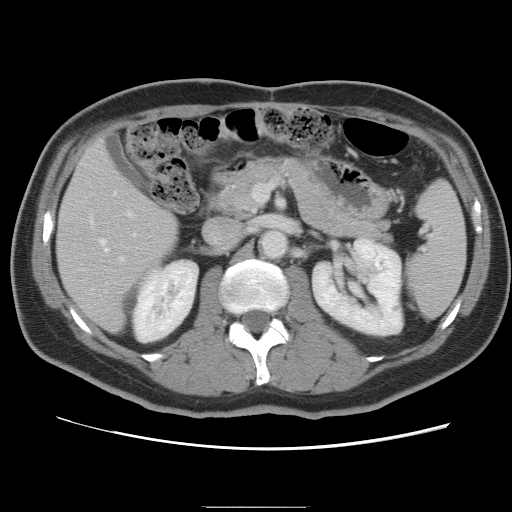
Contrast-enhanced abdominal CT, one axial slice; 120 kVp; intravenous contrast given; soft-tissue window (W 400 / L 40 HU); 5 mm slice thickness; 512 × 512 image matrix. Male patient, age 63 years. From the clinical record (not read from this slice): diagnosis: colorectal cancer liver metastases, imaged before liver resection; multiple liver metastases: no; largest metastasis: 9 cm.
Outlined on this slice (expert manual segmentation):
- hepatic veins: bounding box (x1, y1, x2, y2) in pixels: (100, 192, 116, 251)
- liver: (58, 142, 177, 332)
- planned liver remnant (the part of the liver to remain after resection): (58, 143, 177, 332)
- portal vein (with intrahepatic branches): (105, 209, 135, 293)